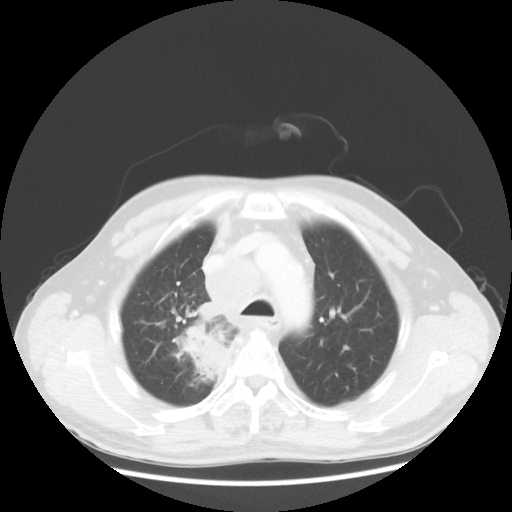
Chest CT, one axial slice; slice 94 of 124 in the series (ordered by position); reconstruction kernel STANDARD; 100 kVp; lung window (W 1500 / L -600 HU); 512 × 512 image matrix, field of view 382 × 382 mm. Male patient, age 64 years. Case-level facts recorded for this patient, not image findings: clinical TNM (as recorded): T3 N3 M0.
Annotated regions visible in this slice (bounding box drawn by a radiologist):
- lung tumour (recorded histology: small cell carcinoma): box from (x=166, y=290) to (x=254, y=389) px